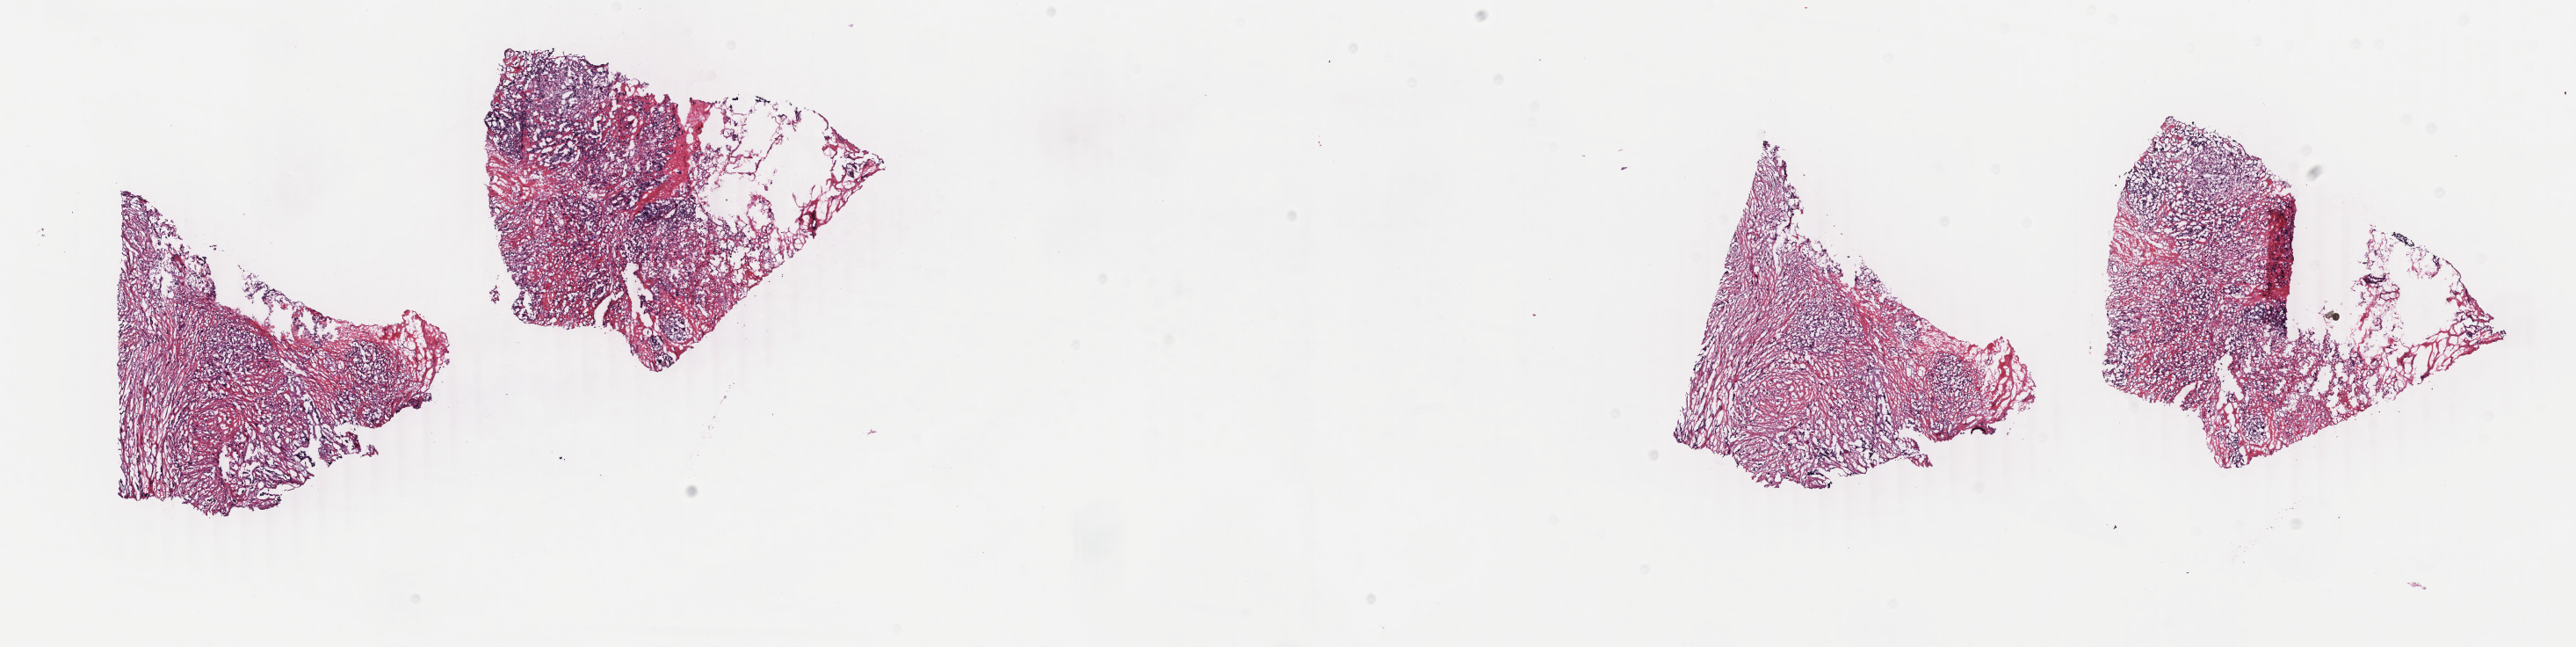
Hematoxylin and eosin (H&E) stained whole-slide image — low-resolution overview of the scanned area, about 23.3 x 5.9 mm (slide scanned at 40x). Frozen section from the bottom of the tissue portion. Primary tumour sample from the breast. Female patient; age at initial diagnosis 60 years. Composition of this section per pathologist review: tumour cells 80%, tumour nuclei 85%, normal cells 0%, stromal cells 20%, necrosis 0%. Infiltration values recorded for this section: lymphocyte infiltration 2%, monocyte infiltration 0%, neutrophil infiltration 0%.
AJCC pathologic stage: IA. Histologic diagnosis: Infiltrating duct carcinoma, NOS. Lymph nodes positive (case pathology): 0 of 19 examined.